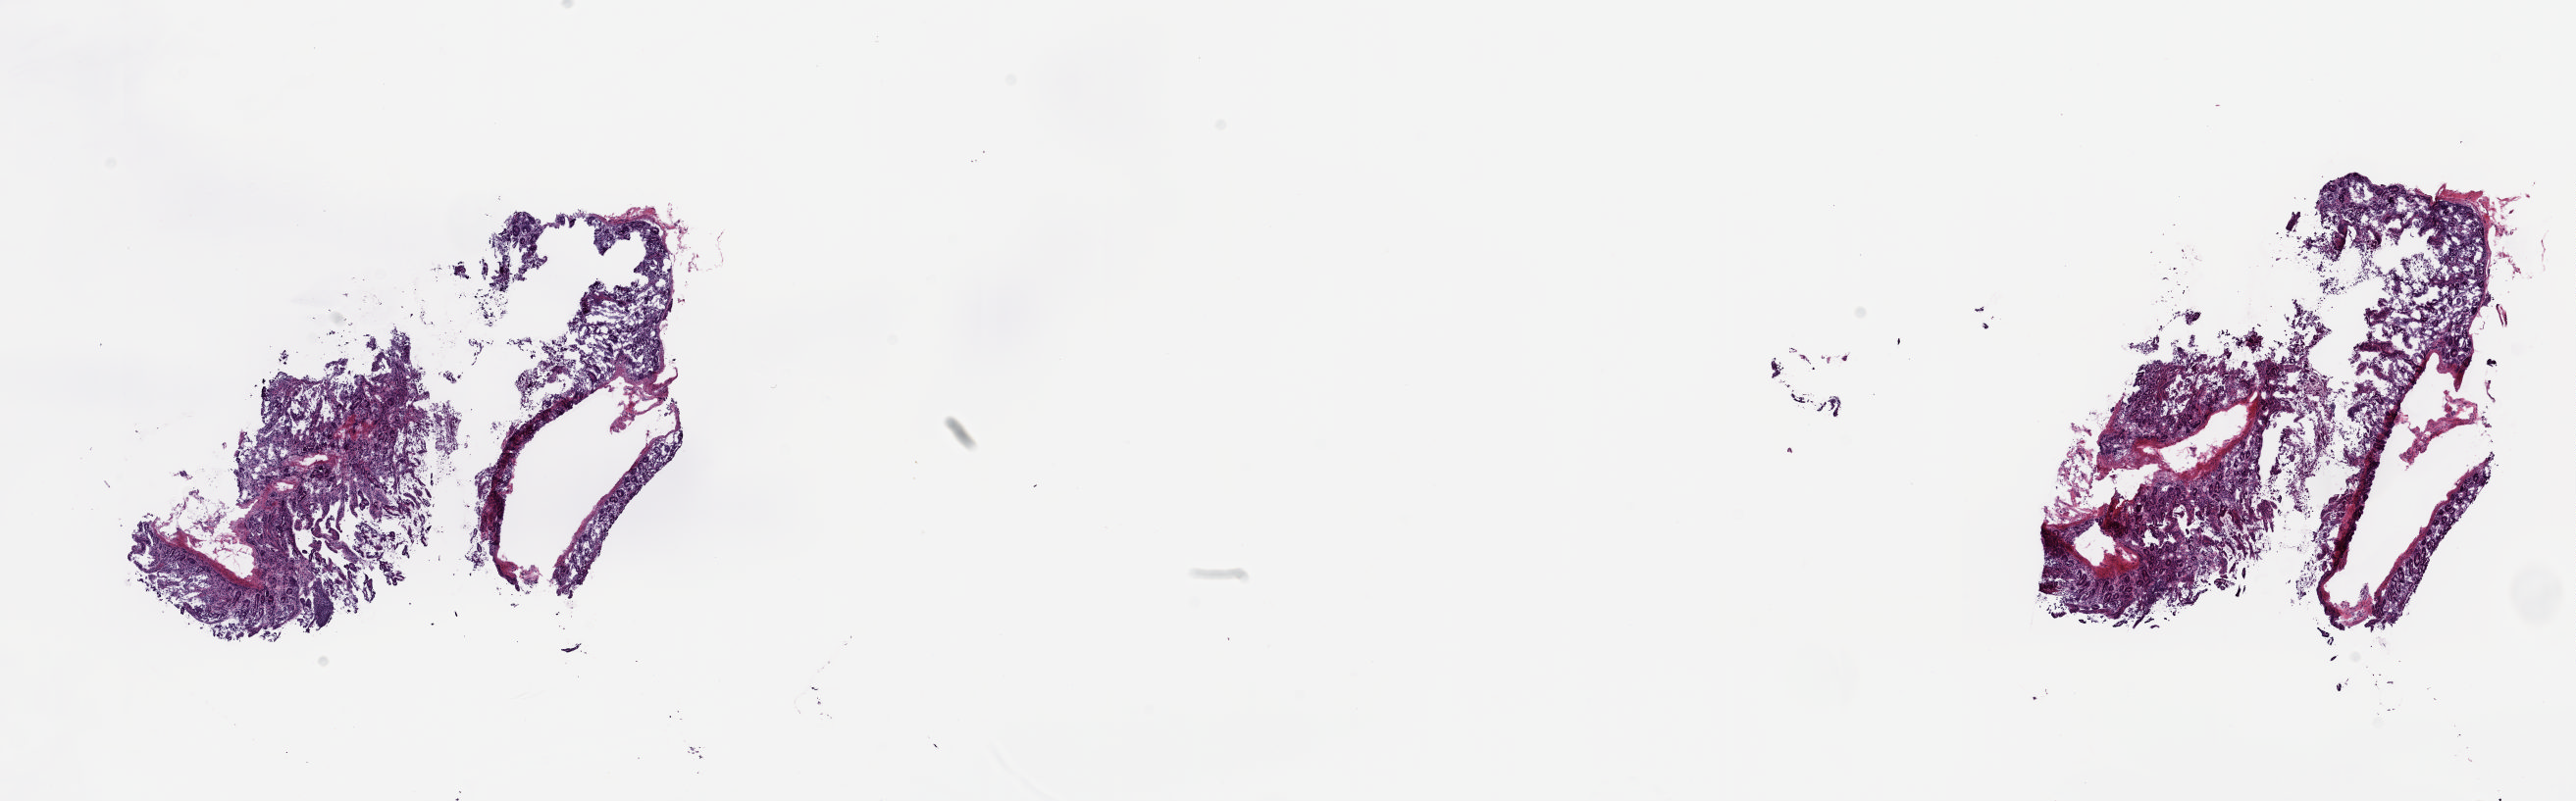
Whole-slide histology image, H&E — a low-resolution overview of the entire scanned area, about 20.8 x 6.5 mm (from a 20x scan). Frozen section. Sample: solid tissue normal (non-tumour tissue), pancreas. Patient: male, age at initial diagnosis 65 years. Slide review estimates, as recorded: tumour cells 0%, tumour nuclei 0%, normal cells 50%, stromal cells 50%, necrosis 0%. Infiltration values recorded for this section: lymphocyte infiltration 70%, monocyte infiltration 10%, neutrophil infiltration 10%.
This section: solid tissue normal sample (biorepository sample class). Patient diagnosis: Infiltrating duct carcinoma, NOS (head of pancreas).